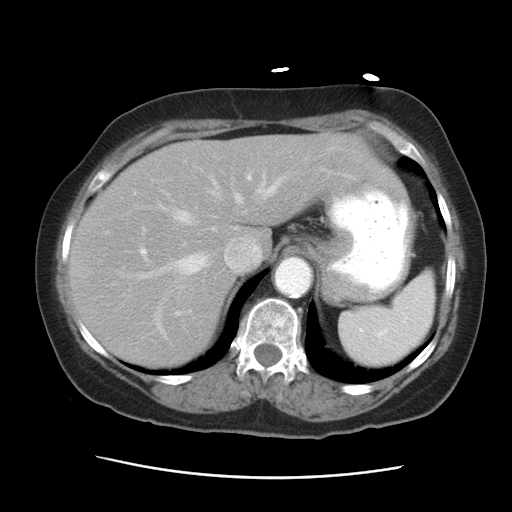
Contrast-enhanced abdominal CT, one axial slice. Slice 22 of 29 in the series (ordered by position). Reconstruction kernel STANDARD. 120 kVp. Intravenous contrast given. Soft-tissue window (W 400 / L 40 HU). 7.5 mm slice thickness. 512 × 512 image matrix. Female patient, age 64 years. From the clinical record (not read from this slice): diagnosis: colorectal cancer liver metastases, imaged before liver resection; multiple liver metastases: no; largest metastasis: 2.5 cm; disease in both lobes: no.
Annotated regions visible in this slice (expert manual segmentation):
- hepatic veins: box from (x=138, y=172) to (x=286, y=337) px
- liver: (x=69, y=132)–(x=375, y=366)
- planned liver remnant (the part of the liver to remain after resection): (x=70, y=132)–(x=376, y=280)
- portal vein (with intrahepatic branches): (x=140, y=247)–(x=147, y=256)